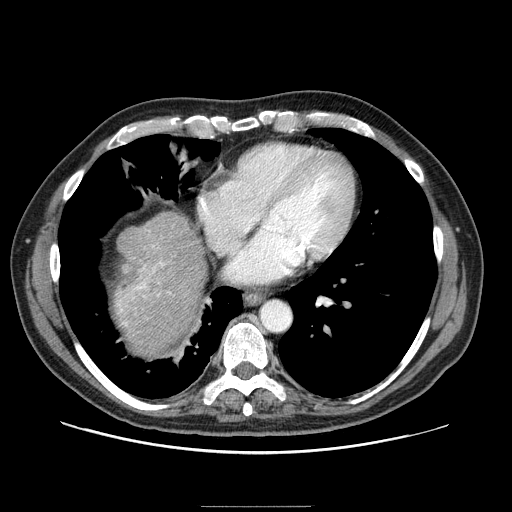
Contrast-enhanced abdominal CT (liver protocol), one axial slice; slice 85 of 99 in the series (ordered by position); reconstruction kernel STANDARD; one of 2 acquisitions stored at this slice position; soft-tissue window (W 400 / L 40 HU); 2.5 mm slice thickness; 512 × 512 image matrix, field of view 400 × 400 mm. From the clinical record (not read from this slice): diagnosis: hepatocellular carcinoma (patient treated with transarterial chemoembolisation; whether this scan precedes or follows treatment is not stated here); TNM stage (as recorded): Stage-II; Child-Pugh class: A; tumour differentiation: well differentiated.
Structures marked on this image (semi-automatic segmentation, software-assisted and operator-edited):
- liver parenchyma outside the tumour (the mass and vessels are separate outlines, so this box may not span the whole liver): bounding box <114,212,206,354> (left, top, right, bottom; pixels)
- liver vessels: <119,262,164,325>